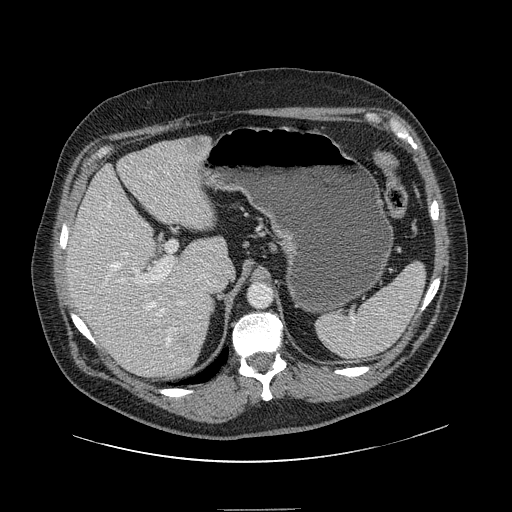
Contrast-enhanced abdominal CT, one axial slice; position 97 of 154 along the scan axis; intravenous contrast given; soft-tissue window (W 400 / L 40 HU); 2.5 mm slice thickness; 512 × 512 image matrix. Male patient, age 61 years. From the clinical record (not read from this slice): diagnosis: colorectal cancer liver metastases, imaged before liver resection; multiple liver metastases: yes; largest metastasis: 2.6 cm; chemotherapy before resection: no.
Outlined on this slice (expert manual segmentation):
- hepatic veins: bounding box (x1, y1, x2, y2) in pixels: (92, 214, 176, 347)
- liver: (69, 137, 226, 379)
- planned liver remnant (the part of the liver to remain after resection): (69, 146, 224, 363)
- portal vein (with intrahepatic branches): (109, 166, 185, 304)
- liver metastasis: (187, 140, 208, 158)